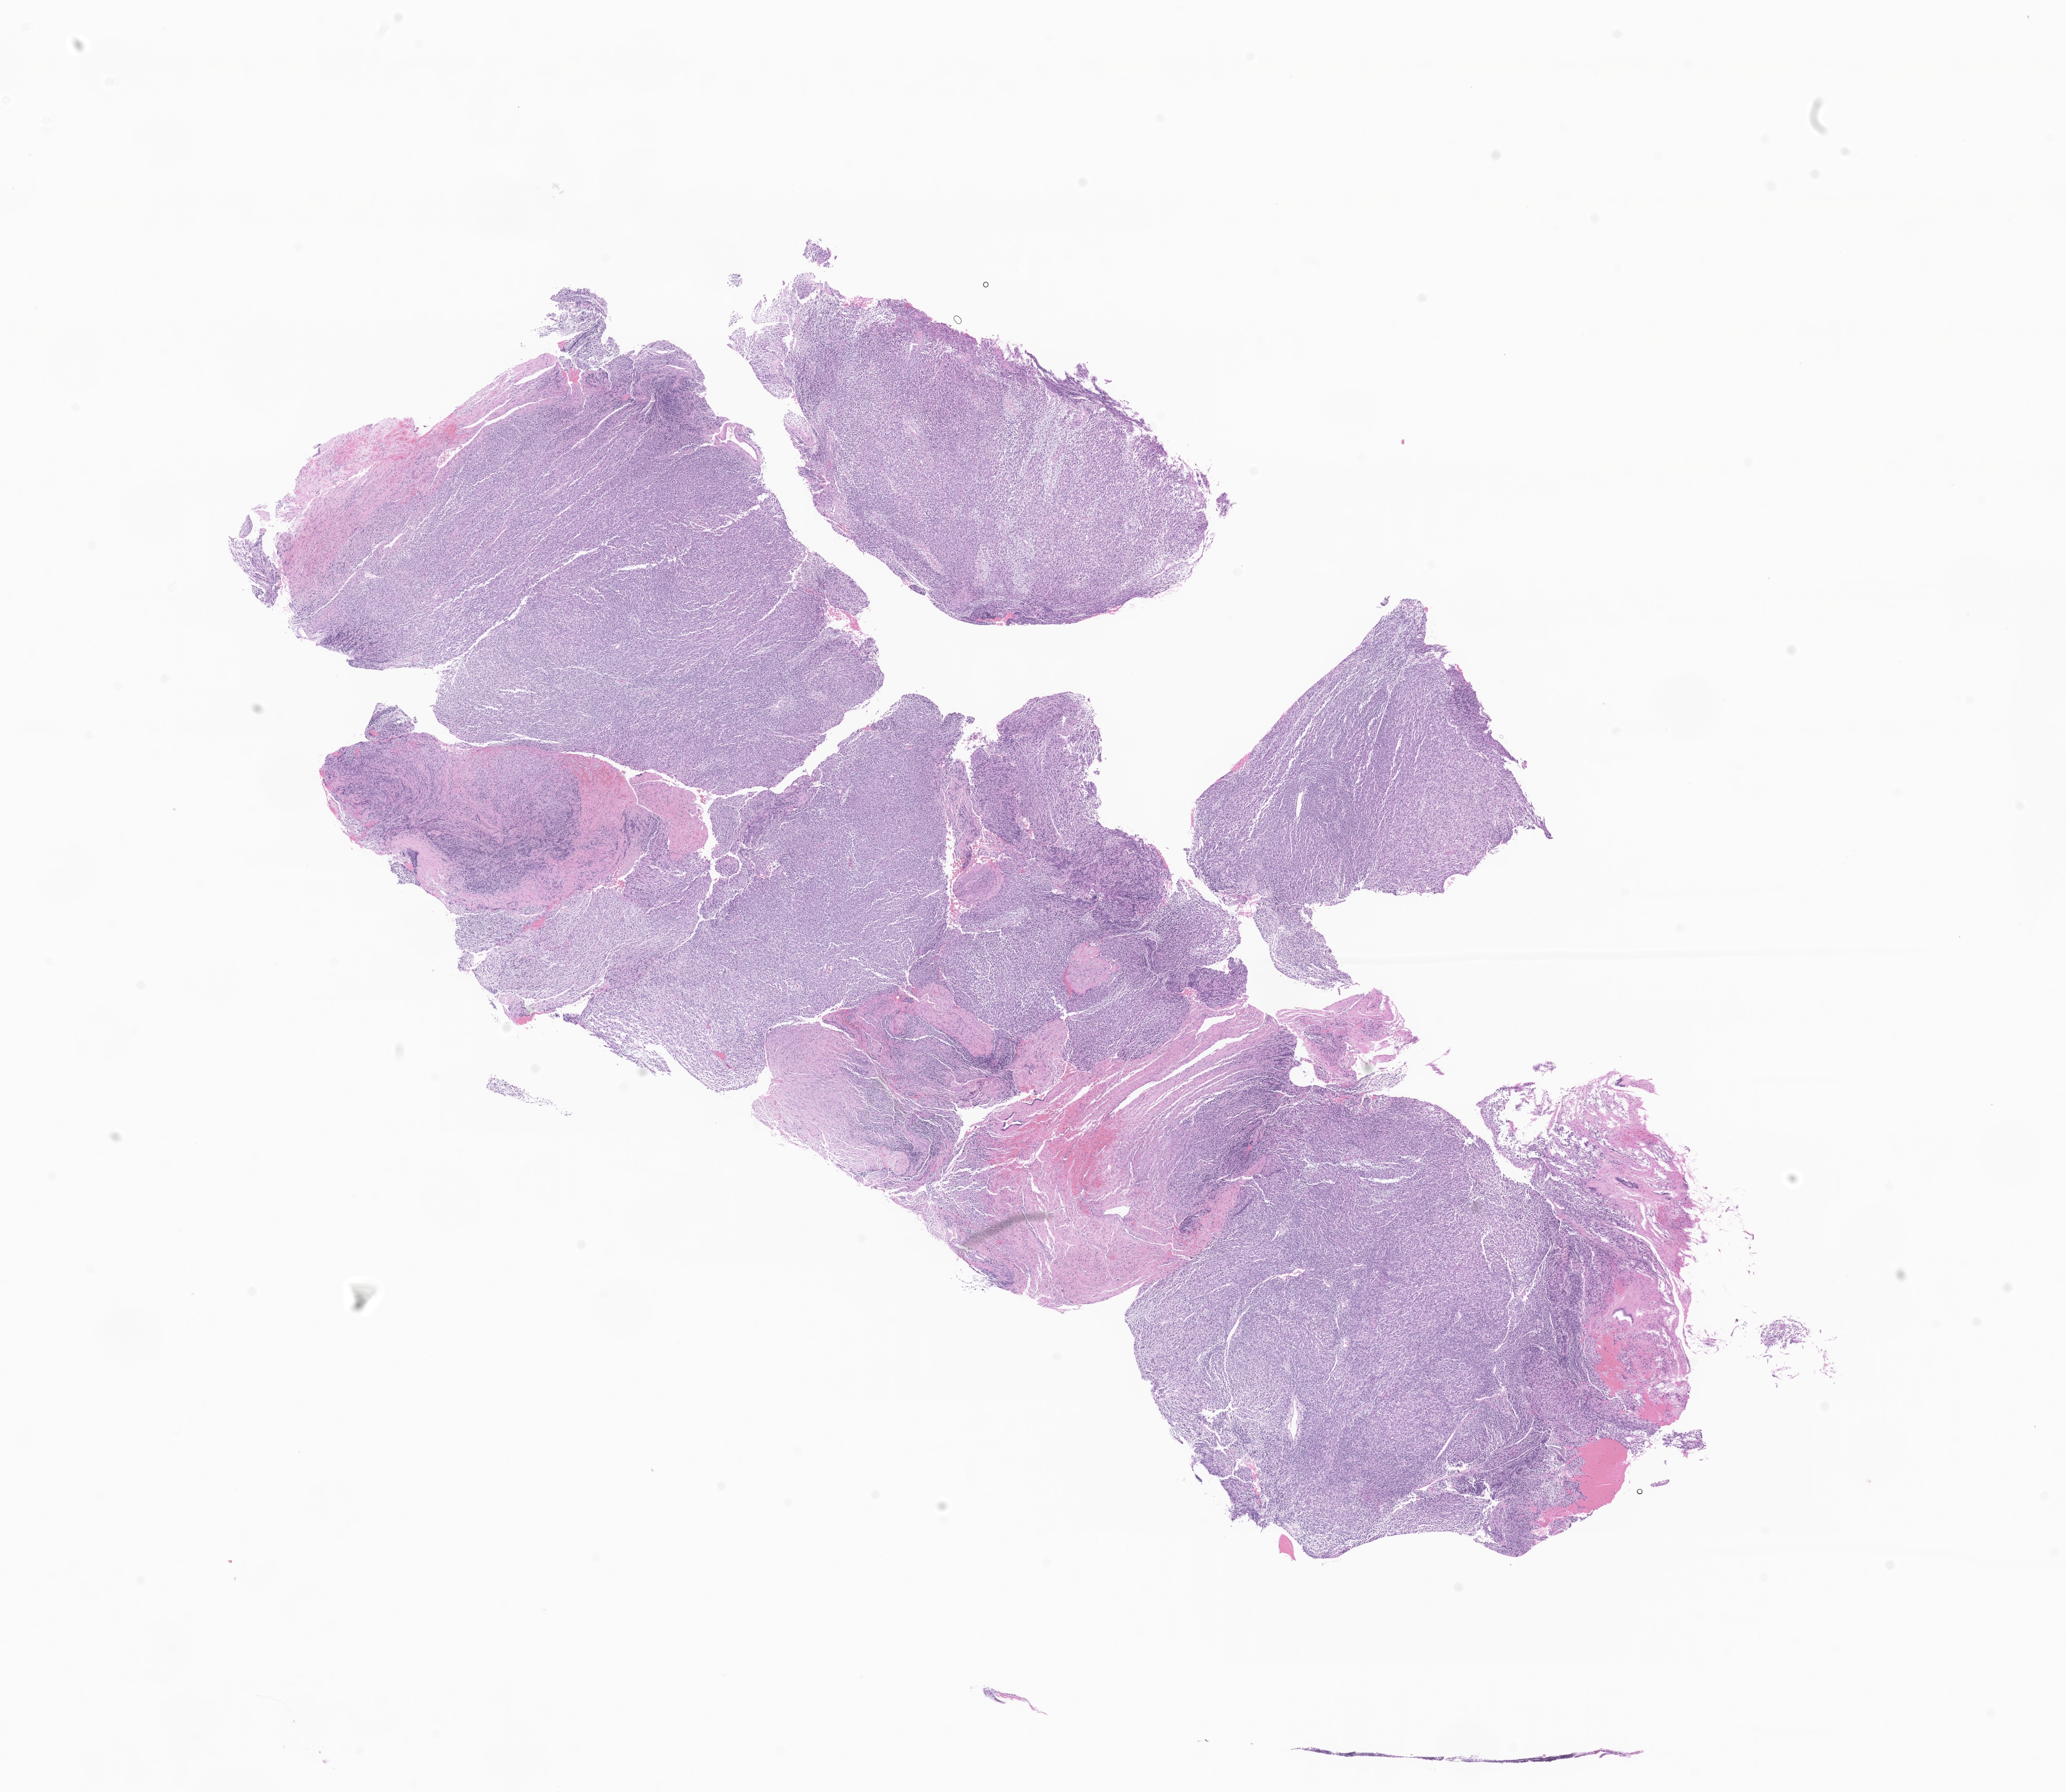
Whole-slide image, H&E stain of tumor tissue from the abdomen — low-resolution overview of the scanned area, about 16.6 x 14.4 mm, formalin-fixed paraffin-embedded section. Patient: male, age 338 days.
Recorded diagnosis: Rhabdomyosarcoma, NOS.